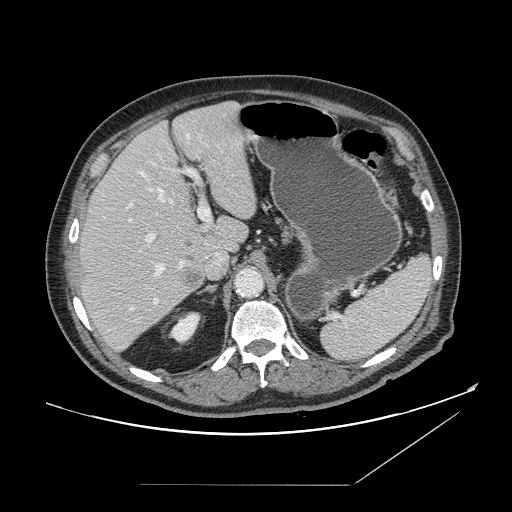
Contrast-enhanced abdominal CT, one axial slice; intravenous contrast given; soft-tissue window (W 400 / L 40 HU); 2.5 mm slice thickness; 512 × 512 image matrix, field of view 416 × 416 mm. Male patient, age 80 years. Case-level facts recorded for this patient, not image findings: diagnosis: colorectal cancer liver metastases, imaged before liver resection; multiple liver metastases: no.
Outlined on this slice (manually delineated by an expert):
- hepatic veins: bounding box (x1, y1, x2, y2) in pixels: (130, 135, 189, 311)
- liver: (80, 102, 257, 352)
- planned liver remnant (the part of the liver to remain after resection): (88, 102, 257, 257)
- portal vein (with intrahepatic branches): (128, 169, 211, 303)
- liver metastasis: (186, 273, 203, 289)
- liver metastasis: (183, 269, 203, 287)